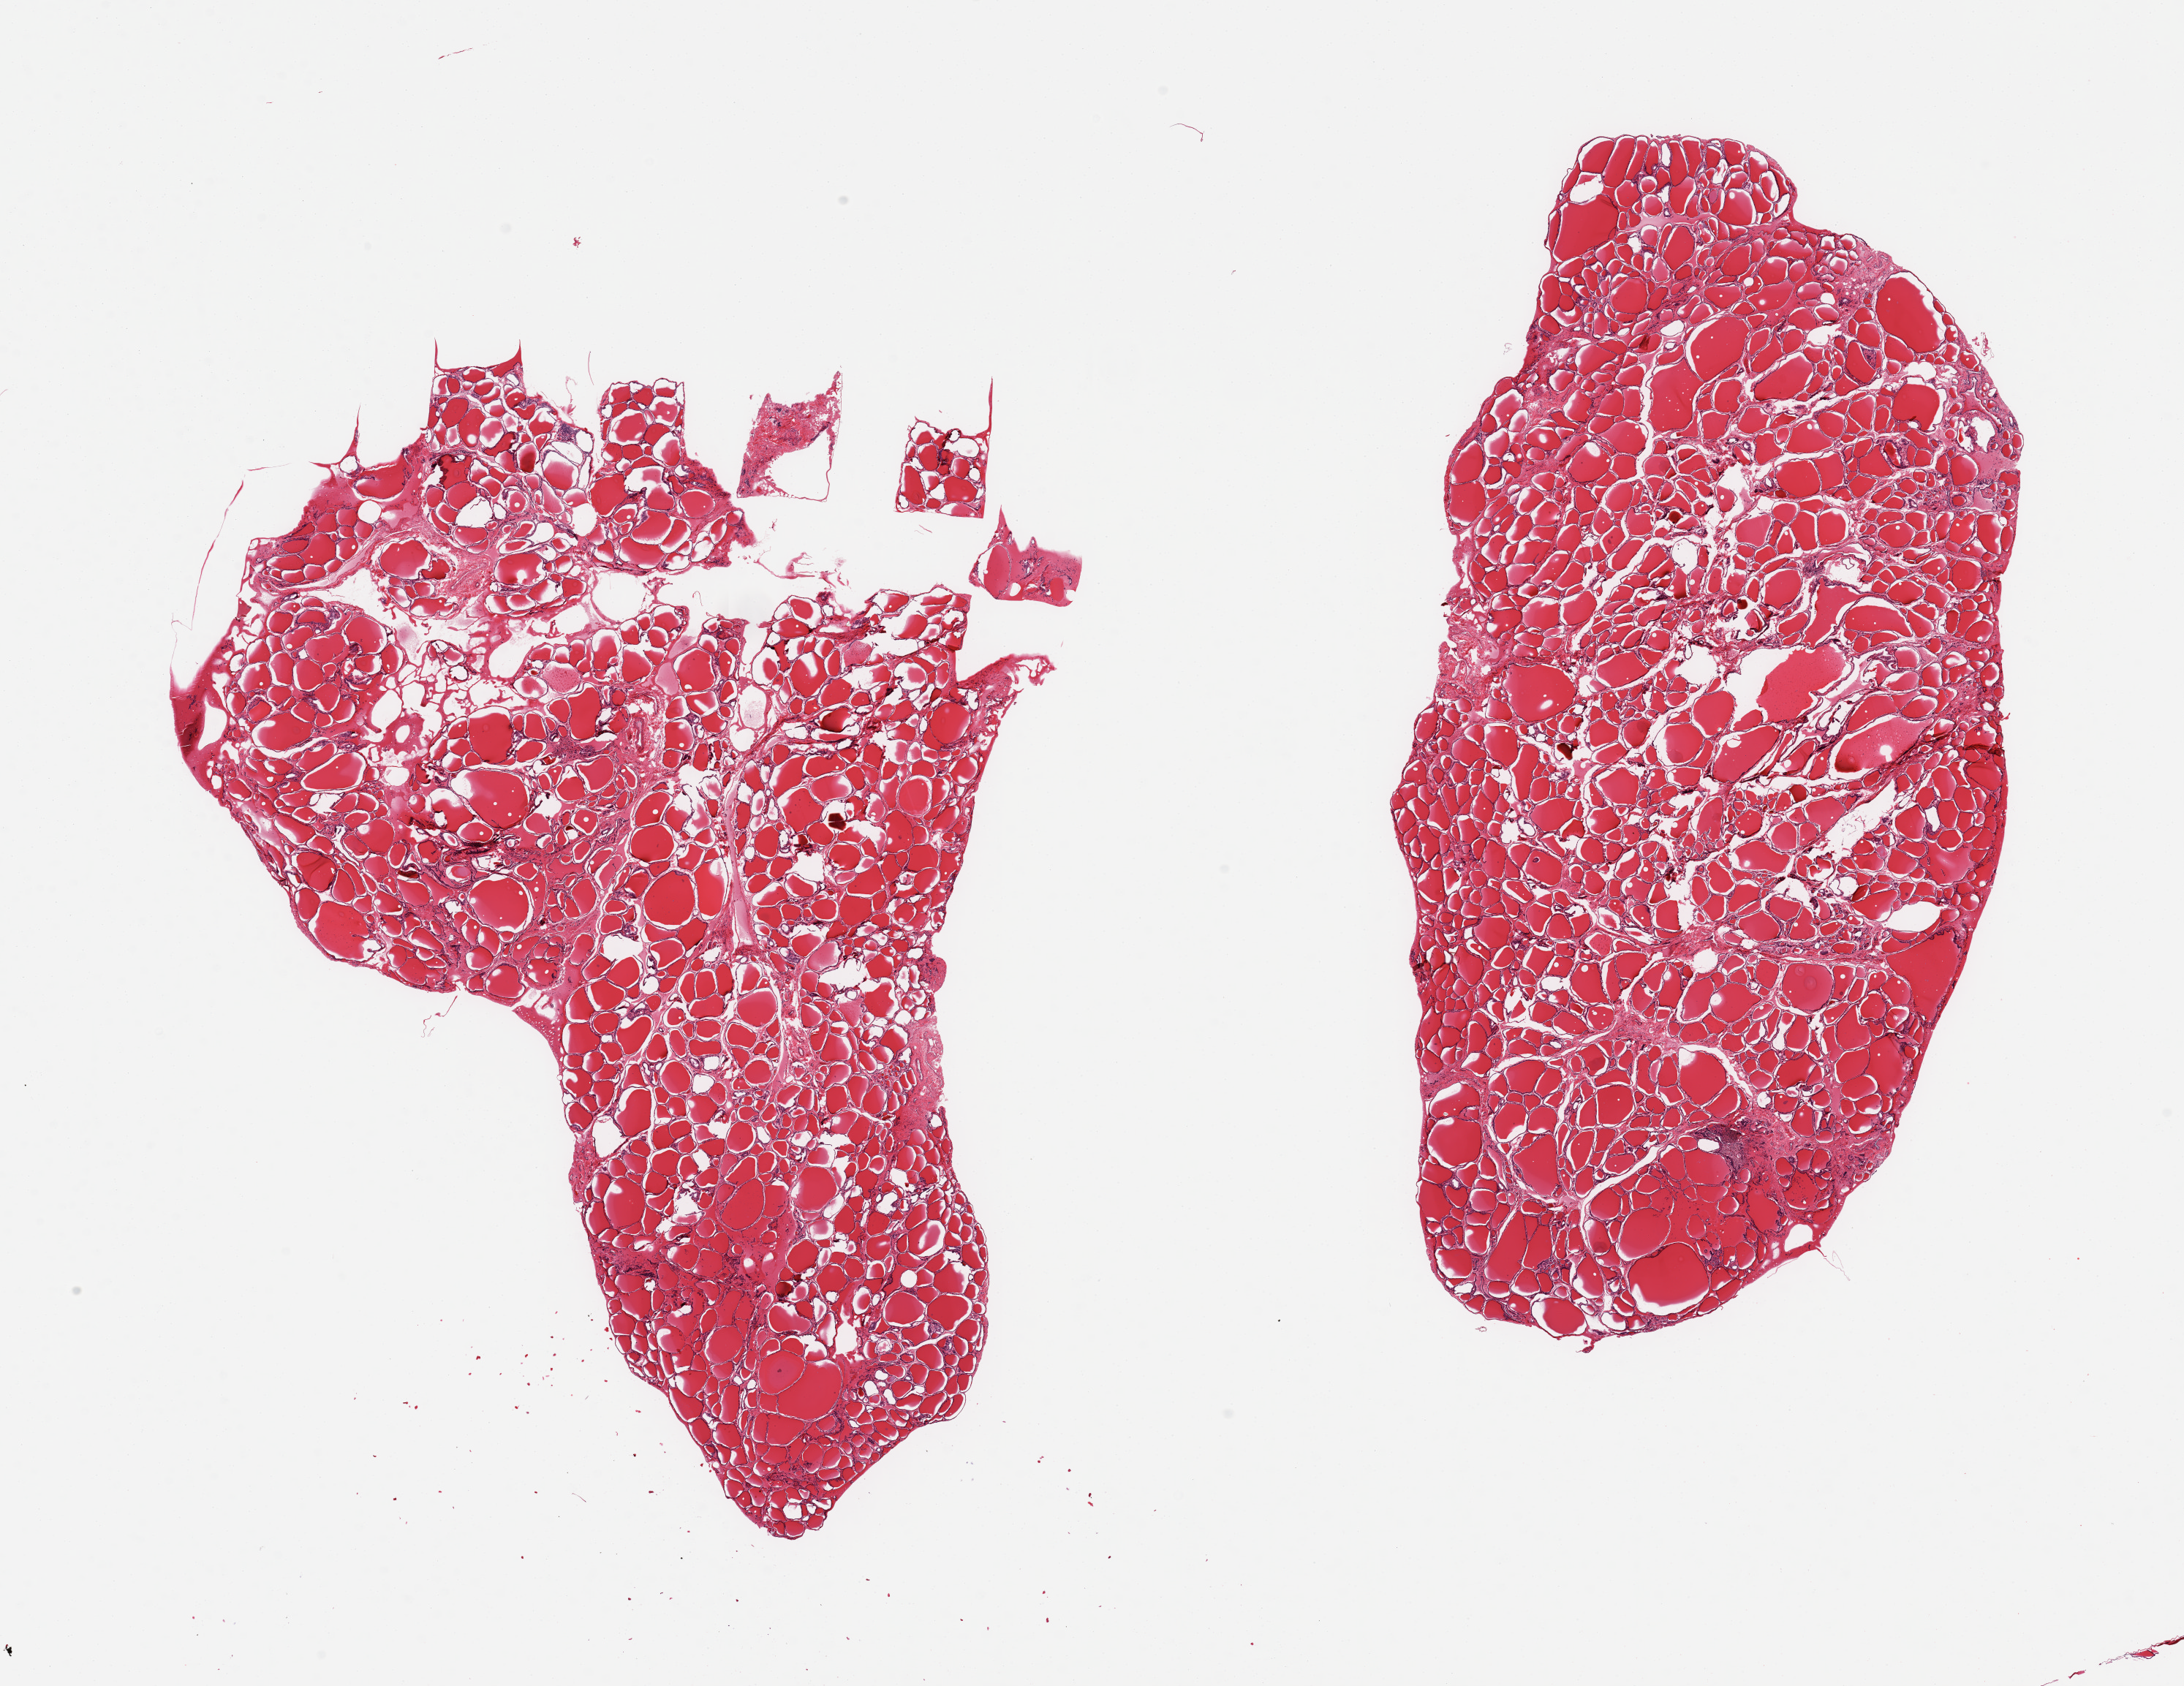
Hematoxylin and eosin (H&E) whole-slide image, brightfield, shown as a low-resolution overview of the whole scanned area (about 23.6 x 18.2 mm), PAXgene-fixed paraffin-embedded (PFPE) section, target tissue: thyroid, donor tissue sample. Male donor.
Review note (as recorded): 2 pieces.